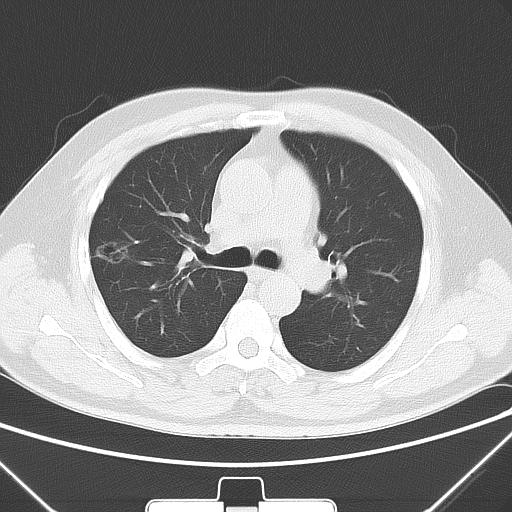
Chest CT, one axial slice; slice 40 of 64 in the series (ordered by position); 120 kVp; lung window (W 1500 / L -600 HU); 5 mm slice thickness; 512 × 512 image matrix. Patient: male, 58 years. Case-level facts recorded for this patient, not image findings: clinical TNM (as recorded): T1c N0 M0; histopathological grade: G2.
Annotated regions visible in this slice (bounding box drawn by a radiologist):
- lung tumour (recorded histology: adenocarcinoma): bounding box [x1, y1, x2, y2] px = [89, 231, 129, 277]